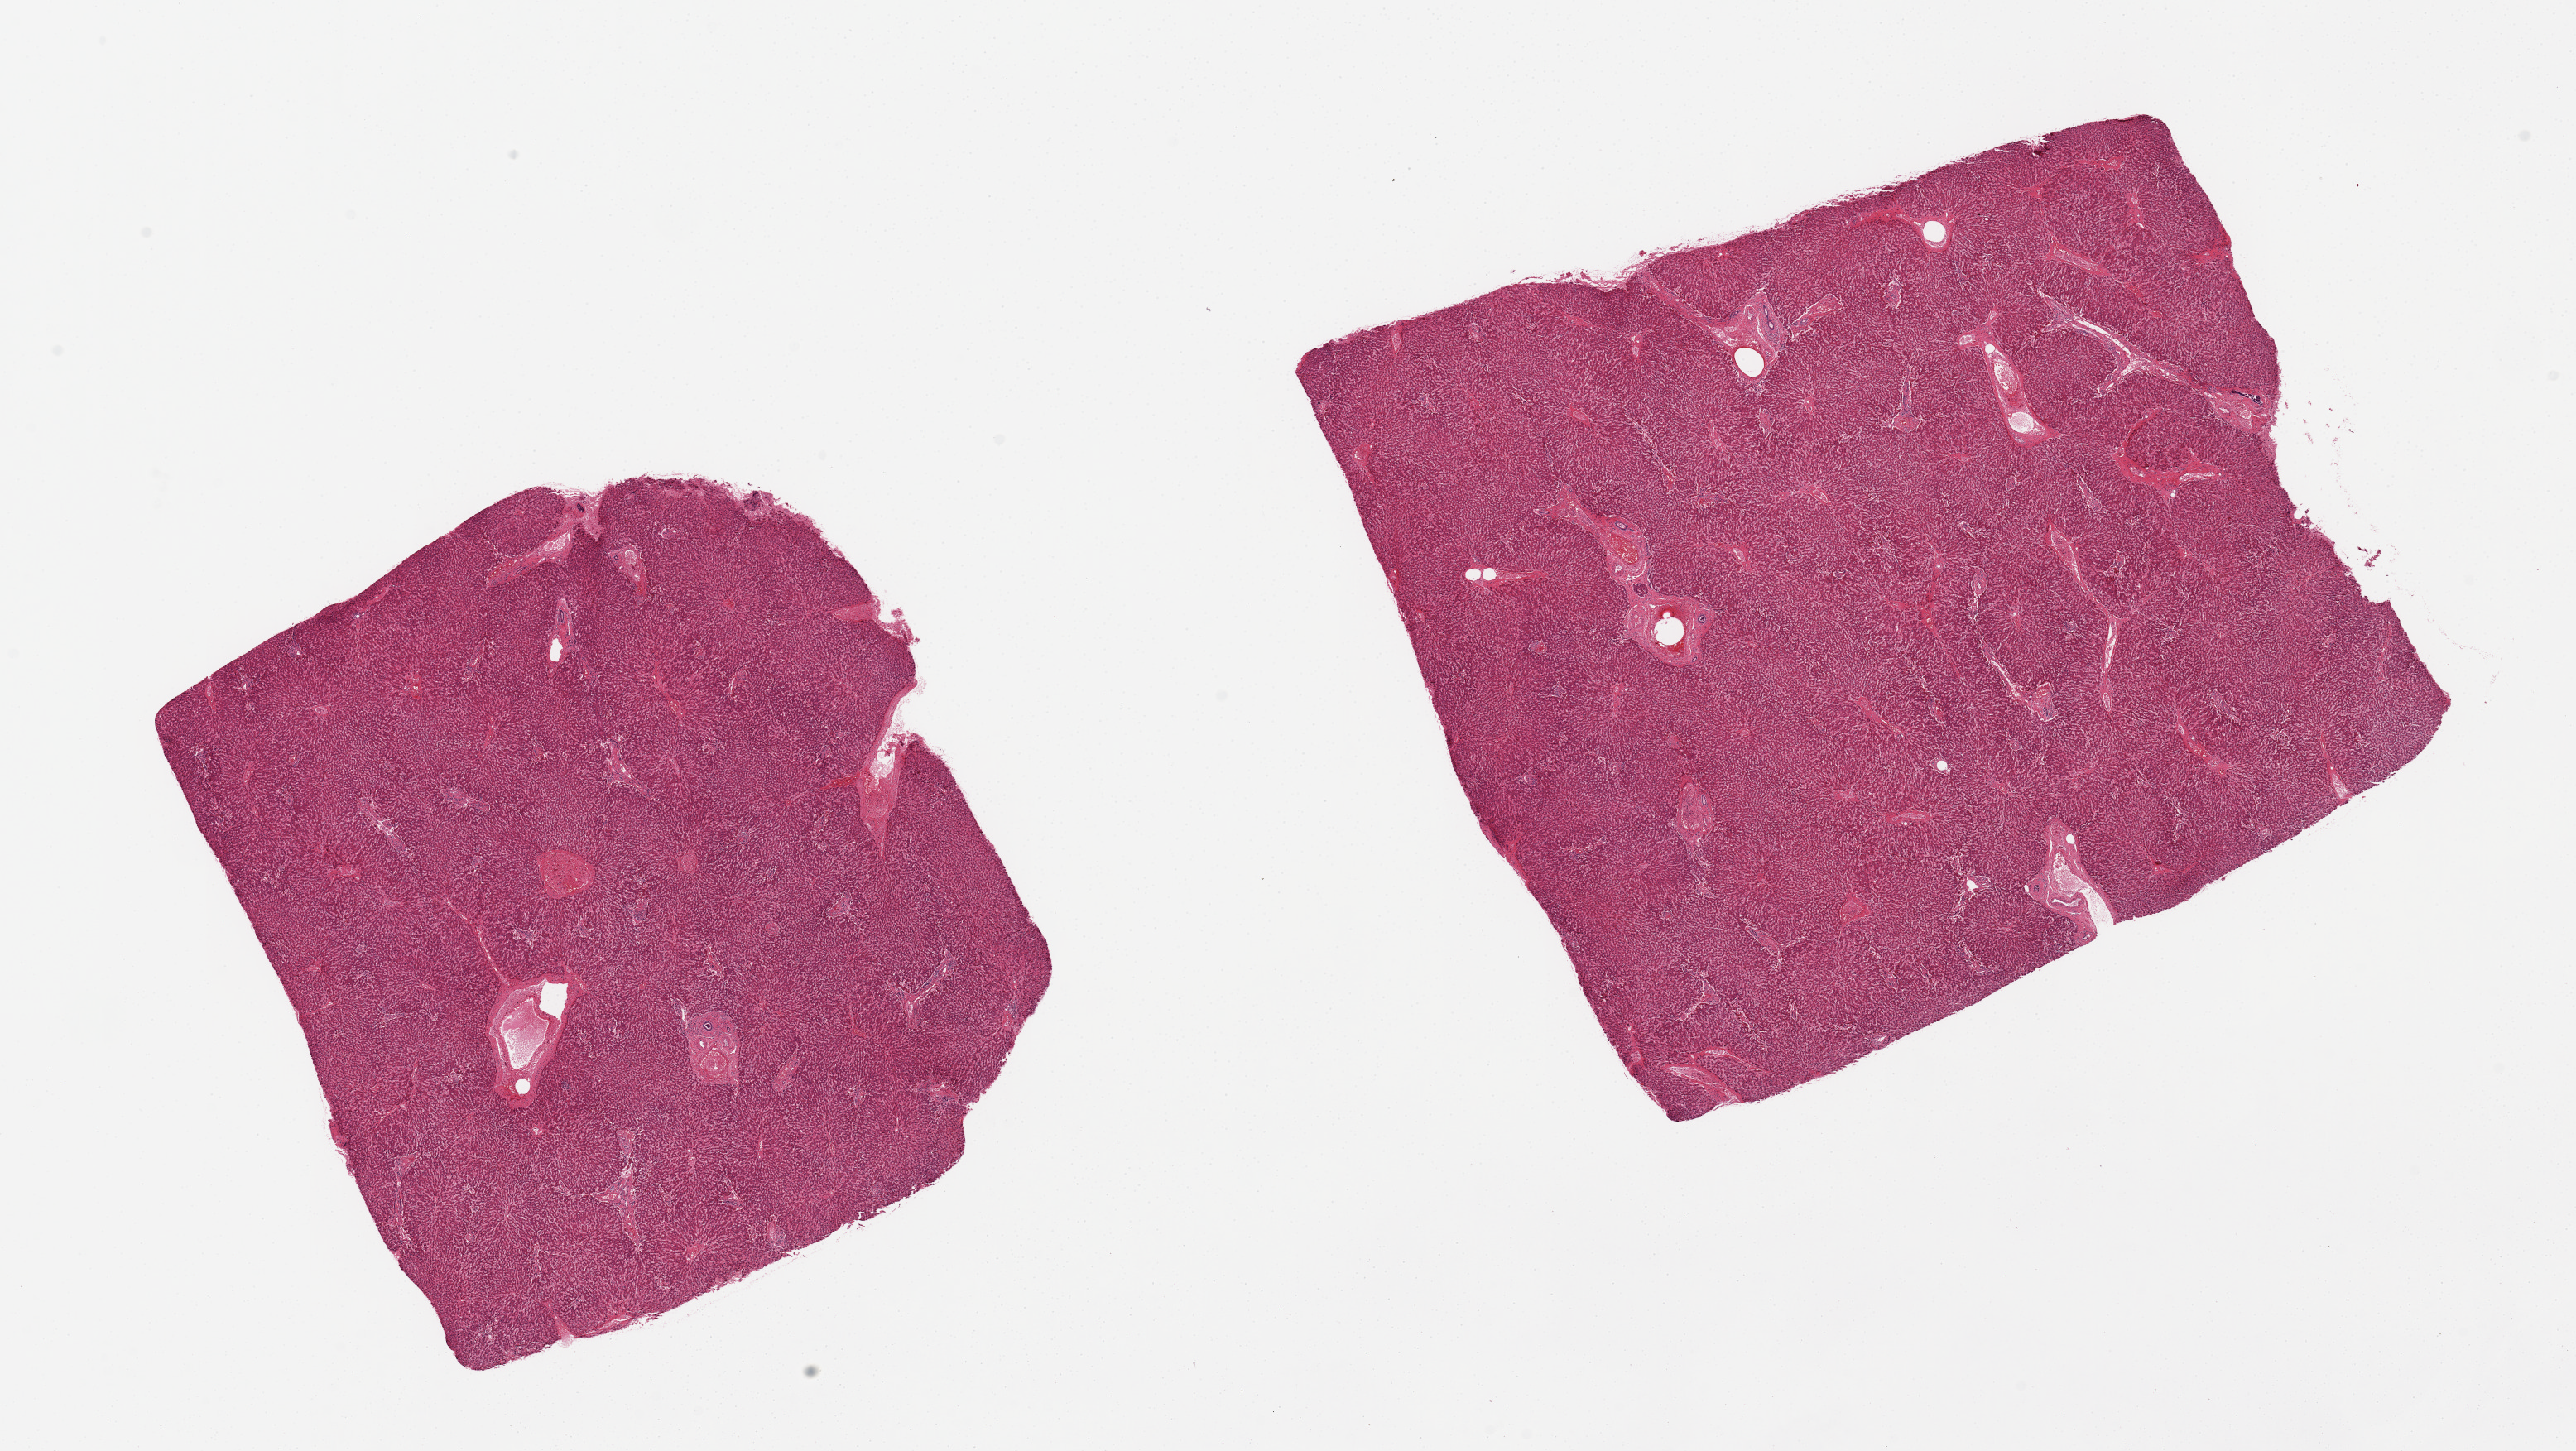
Whole-slide image, H&E stain — whole scanned area (about 24.6 x 13.9 mm) shown as a low-resolution overview. PAXgene-fixed, paraffin-embedded tissue. Target tissue: liver. Tissue donor sample. Donor sex: female.
Pathologist's review note for this sample: 2 pieces, minimal steatosis, moderate autolysis.